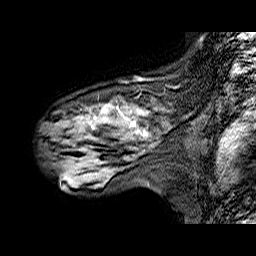
Breast MRI (dynamic contrast-enhanced), one sagittal slice. Slice 43 of 60 in the series (ordered by position). Dynamic contrast-enhanced series, time point 2 of 6 at this slice position (early post-contrast). 1.5 T. TE 6.3 ms, TR 32.9 ms. 4 mm slice thickness. 256 × 256 image matrix, field of view 200 × 200 mm. Female patient. Case-level facts recorded for this patient, not image findings: setting: breast cancer imaged before/during neoadjuvant chemotherapy; receptor status: HER2-positive.
Annotated regions visible in this slice (semi-automatically segmented with operator editing):
- analysis volume of interest (the breast-tissue region the enhancement analysis was run in; not a lesion): box from (x=45, y=89) to (x=174, y=173) px
- tumour enhancement mask (voxels above the 100 % enhancement threshold inside the analysis volume of interest): (x=101, y=108)–(x=148, y=138)